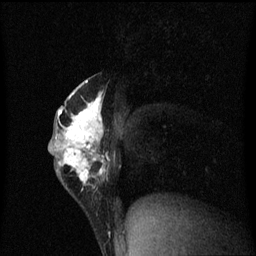
Breast MRI (dynamic contrast-enhanced), one sagittal slice. Slice 32 of 60 in the series (ordered by position). Dynamic contrast-enhanced series, image 2 of 3 at this slice position (ordered by acquisition). 1.5 T. TE 4.2 ms, TR 8.4 ms. 2 mm slice thickness. 256 × 256 image matrix. Female patient, age 40 years.
Structures marked on this image (semi-automatically segmented with operator editing):
- analysis volume of interest (the breast-tissue region the enhancement analysis was run in; not a lesion): bounding box (x1, y1, x2, y2) in pixels: (50, 76, 112, 201)
- tumour enhancement mask (voxels above the 70 % enhancement threshold inside the analysis volume of interest): (50, 80, 111, 185)